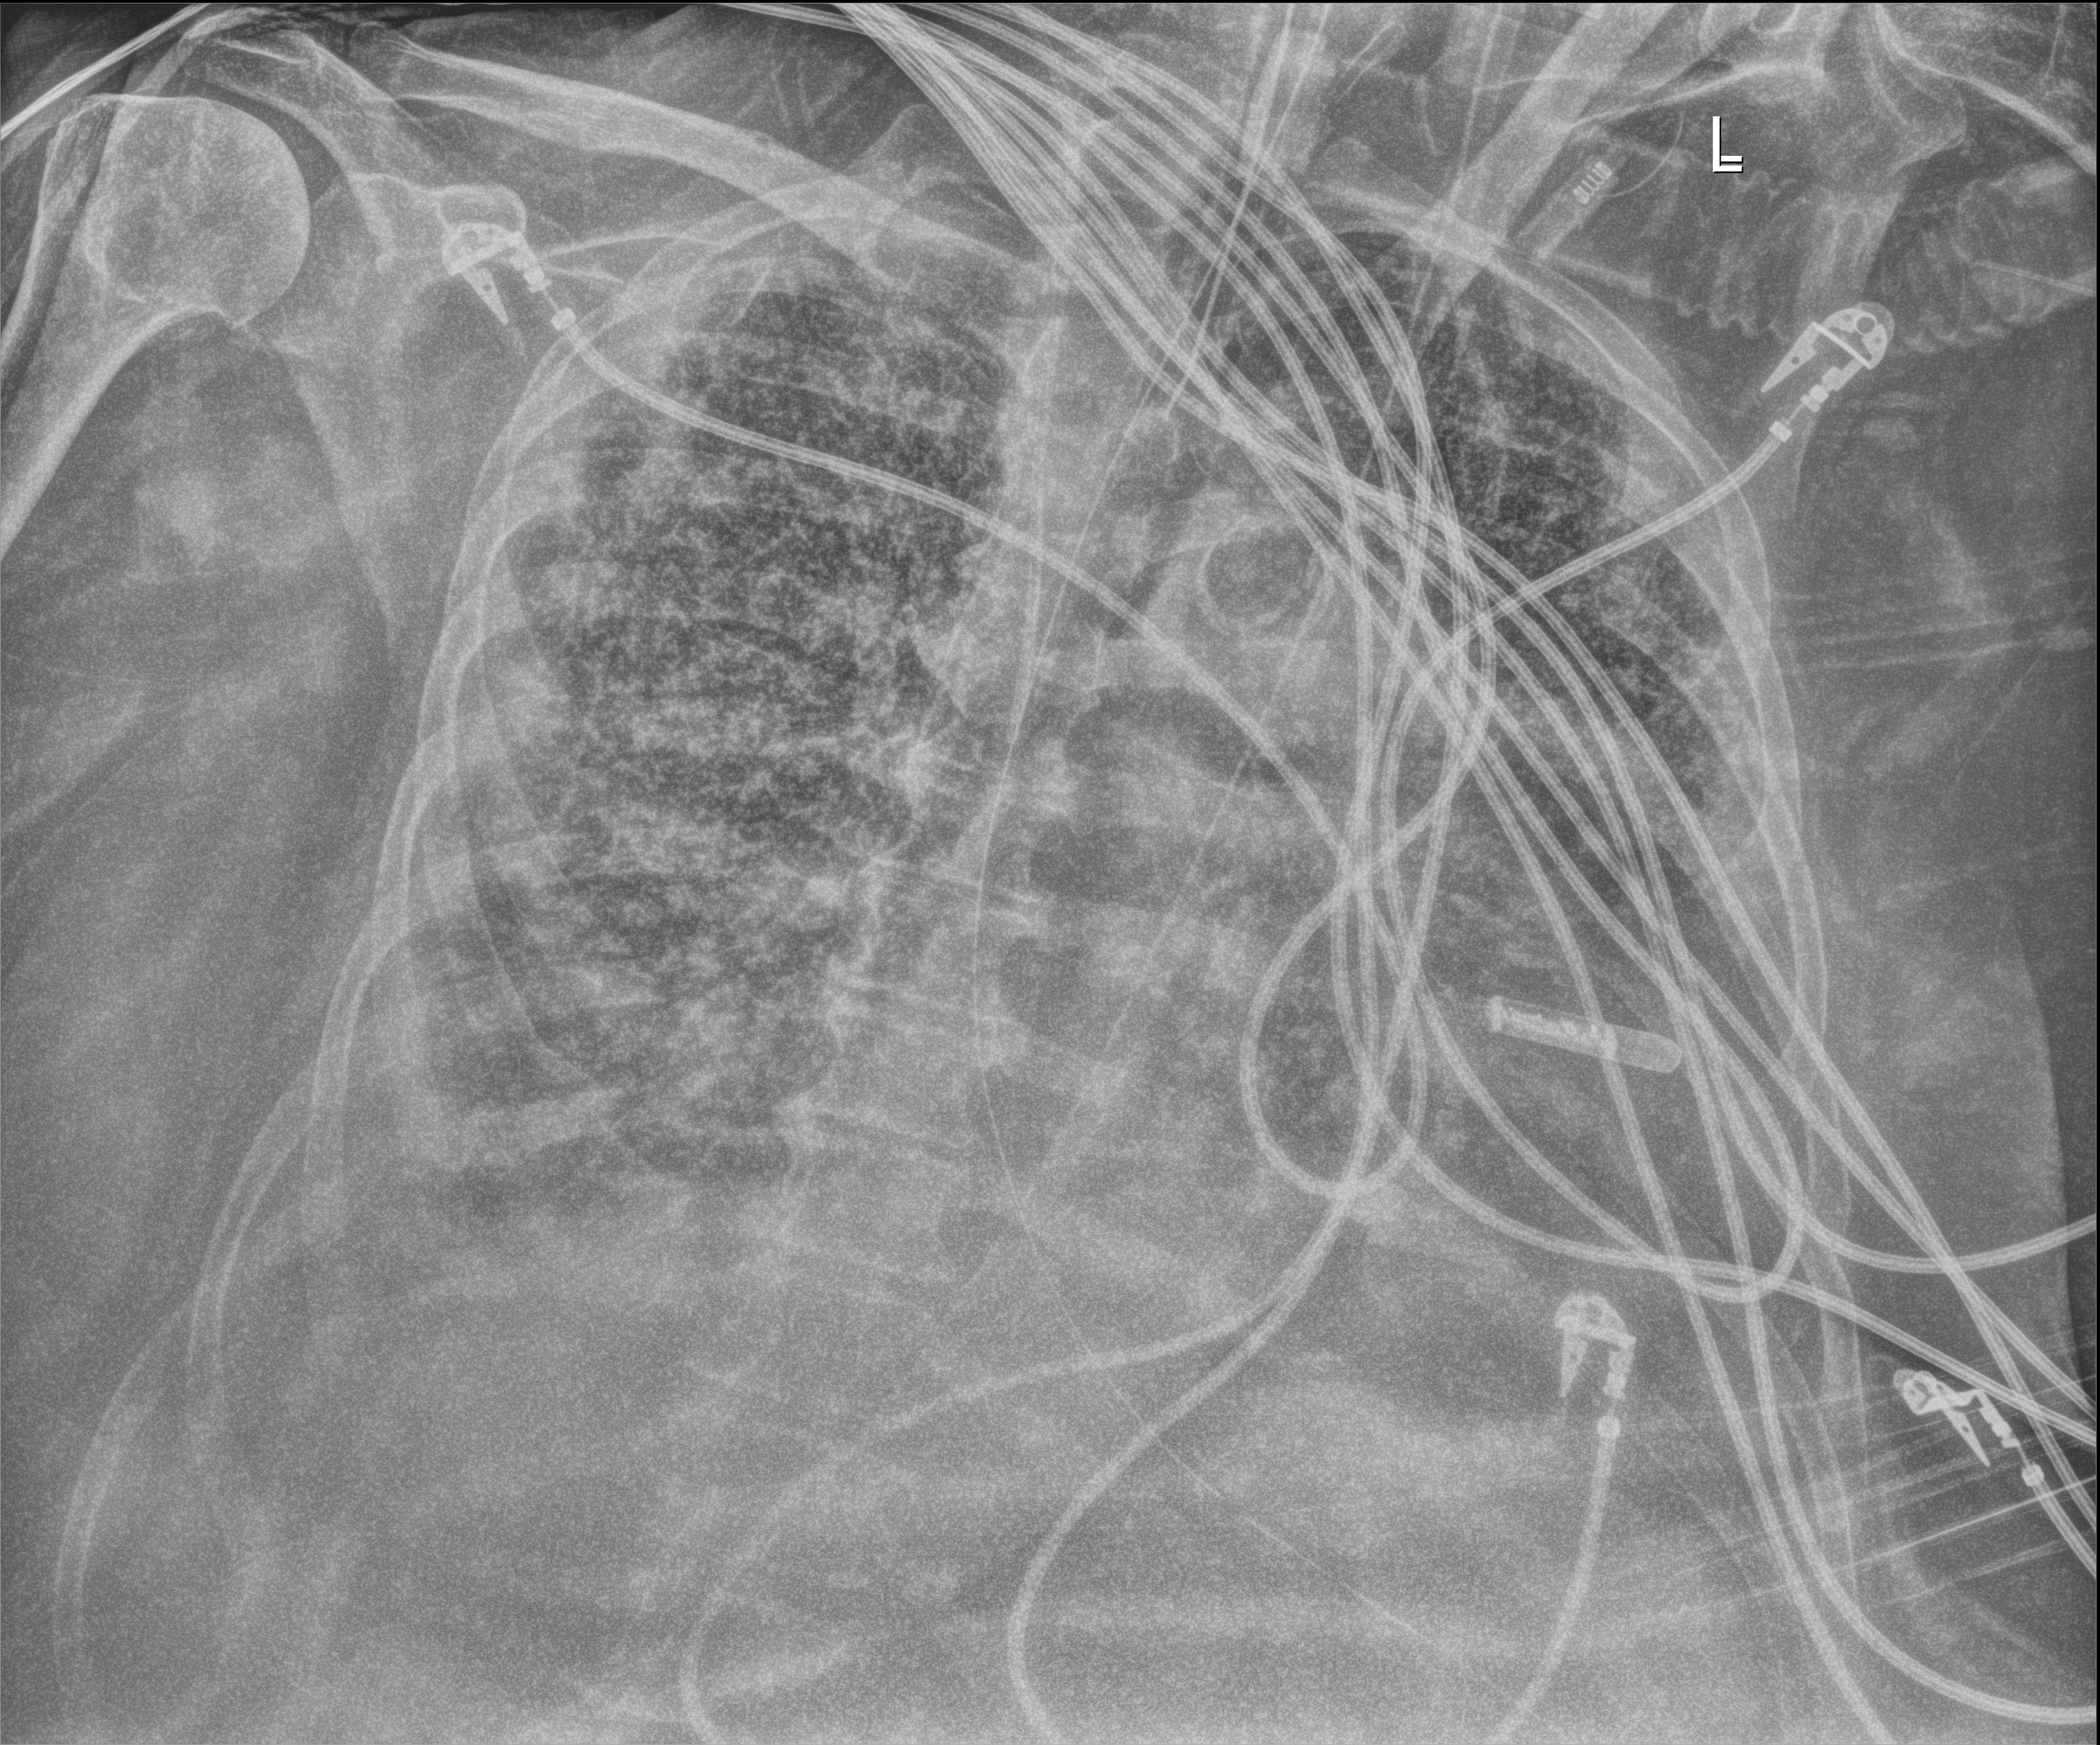
Portable chest radiograph; anteroposterior (AP) projection. Female patient hospitalised with COVID-19, age 60–74 years.
Admission-level facts for this patient (not findings on this image; timing relative to this image not recorded): admitted to intensive care during this hospital stay: yes; hypertension (admission record): yes.